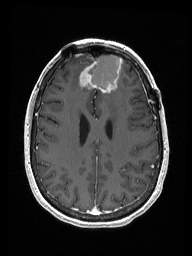
Brain MRI from a brain-tumour surgery series, one axial slice. Slice 61 of 192 in the series (ordered by position). T1-weighted post-contrast. 192 × 256 image matrix. From the clinical record (not read from this slice): histopathology: Metastastic Carcinoma from Breast primary; tumour location: Right Frontal.
Annotated regions visible in this slice (manually delineated by an expert):
- previous resection cavity: bounding box <88,55,123,90> (left, top, right, bottom; pixels)